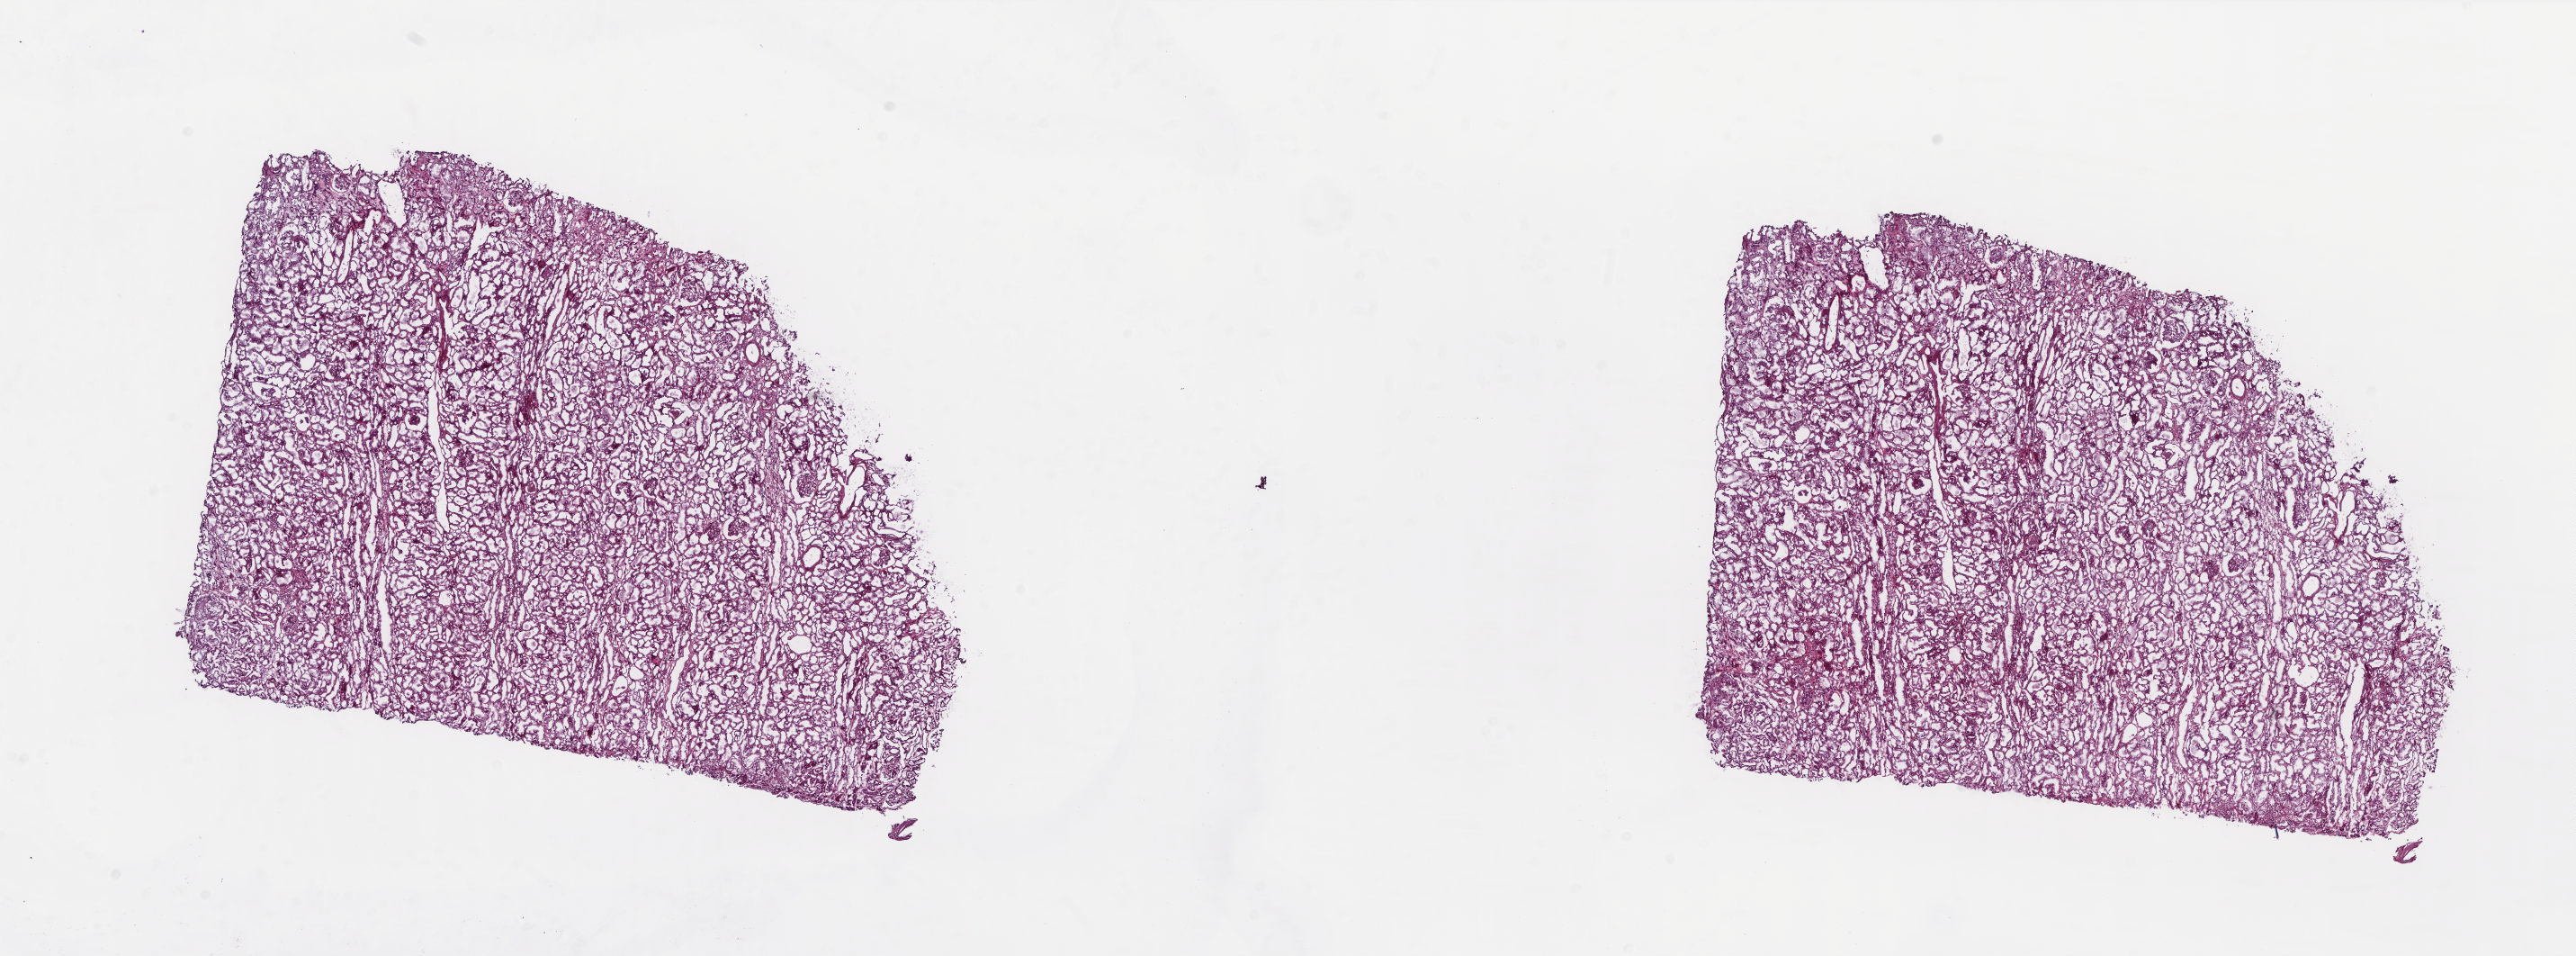
H&E-stained whole-slide image — low-resolution overview of the scanned area, about 23.1 x 8.6 mm (acquisition: 20x scan). Frozen section from the top of the tissue portion. Solid tissue normal (non-tumour tissue) sample from the adrenal cortex. Female, age 61 years at initial diagnosis. Composition of this section per pathologist review: tumour cells 0%, tumour nuclei 0%, normal cells 100%, stromal cells 0%, necrosis 0%. Infiltration values recorded for this section: lymphocyte infiltration 0%, monocyte infiltration 0%, neutrophil infiltration 0%.
This section: solid tissue normal (non-tumour) sample from the same patient. Patient diagnosis: Adrenal cortical carcinoma (cortex of adrenal gland).